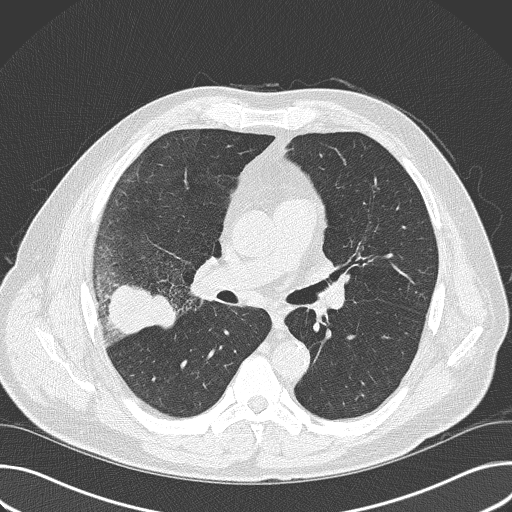
Axial slice from a low-dose chest CT screening exam. Baseline annual screen. Lung window (W 1500 / L -600 HU). Lung (sharp) reconstruction kernel (B50f). 512 × 512 image matrix. Male participant, aged 56 years at enrolment. Current smoker at enrolment.
Expert reader's lesion annotation, bounding box <80,256,183,359> (left, top, right, bottom; pixels). Reader record for this screening exam (exam-level; its link to the box is not recorded): non-calcified nodule or mass ≥4 mm, right upper lobe, 6 × 5 mm, spiculated (stellate) margins, soft tissue attenuation. Later outcome: lung cancer diagnosed 16 days after this screen — adenocarcinoma, NOS, right upper lobe, poorly differentiated (G3), stage IIB (AJCC 6th edition), 60 mm at pathology.